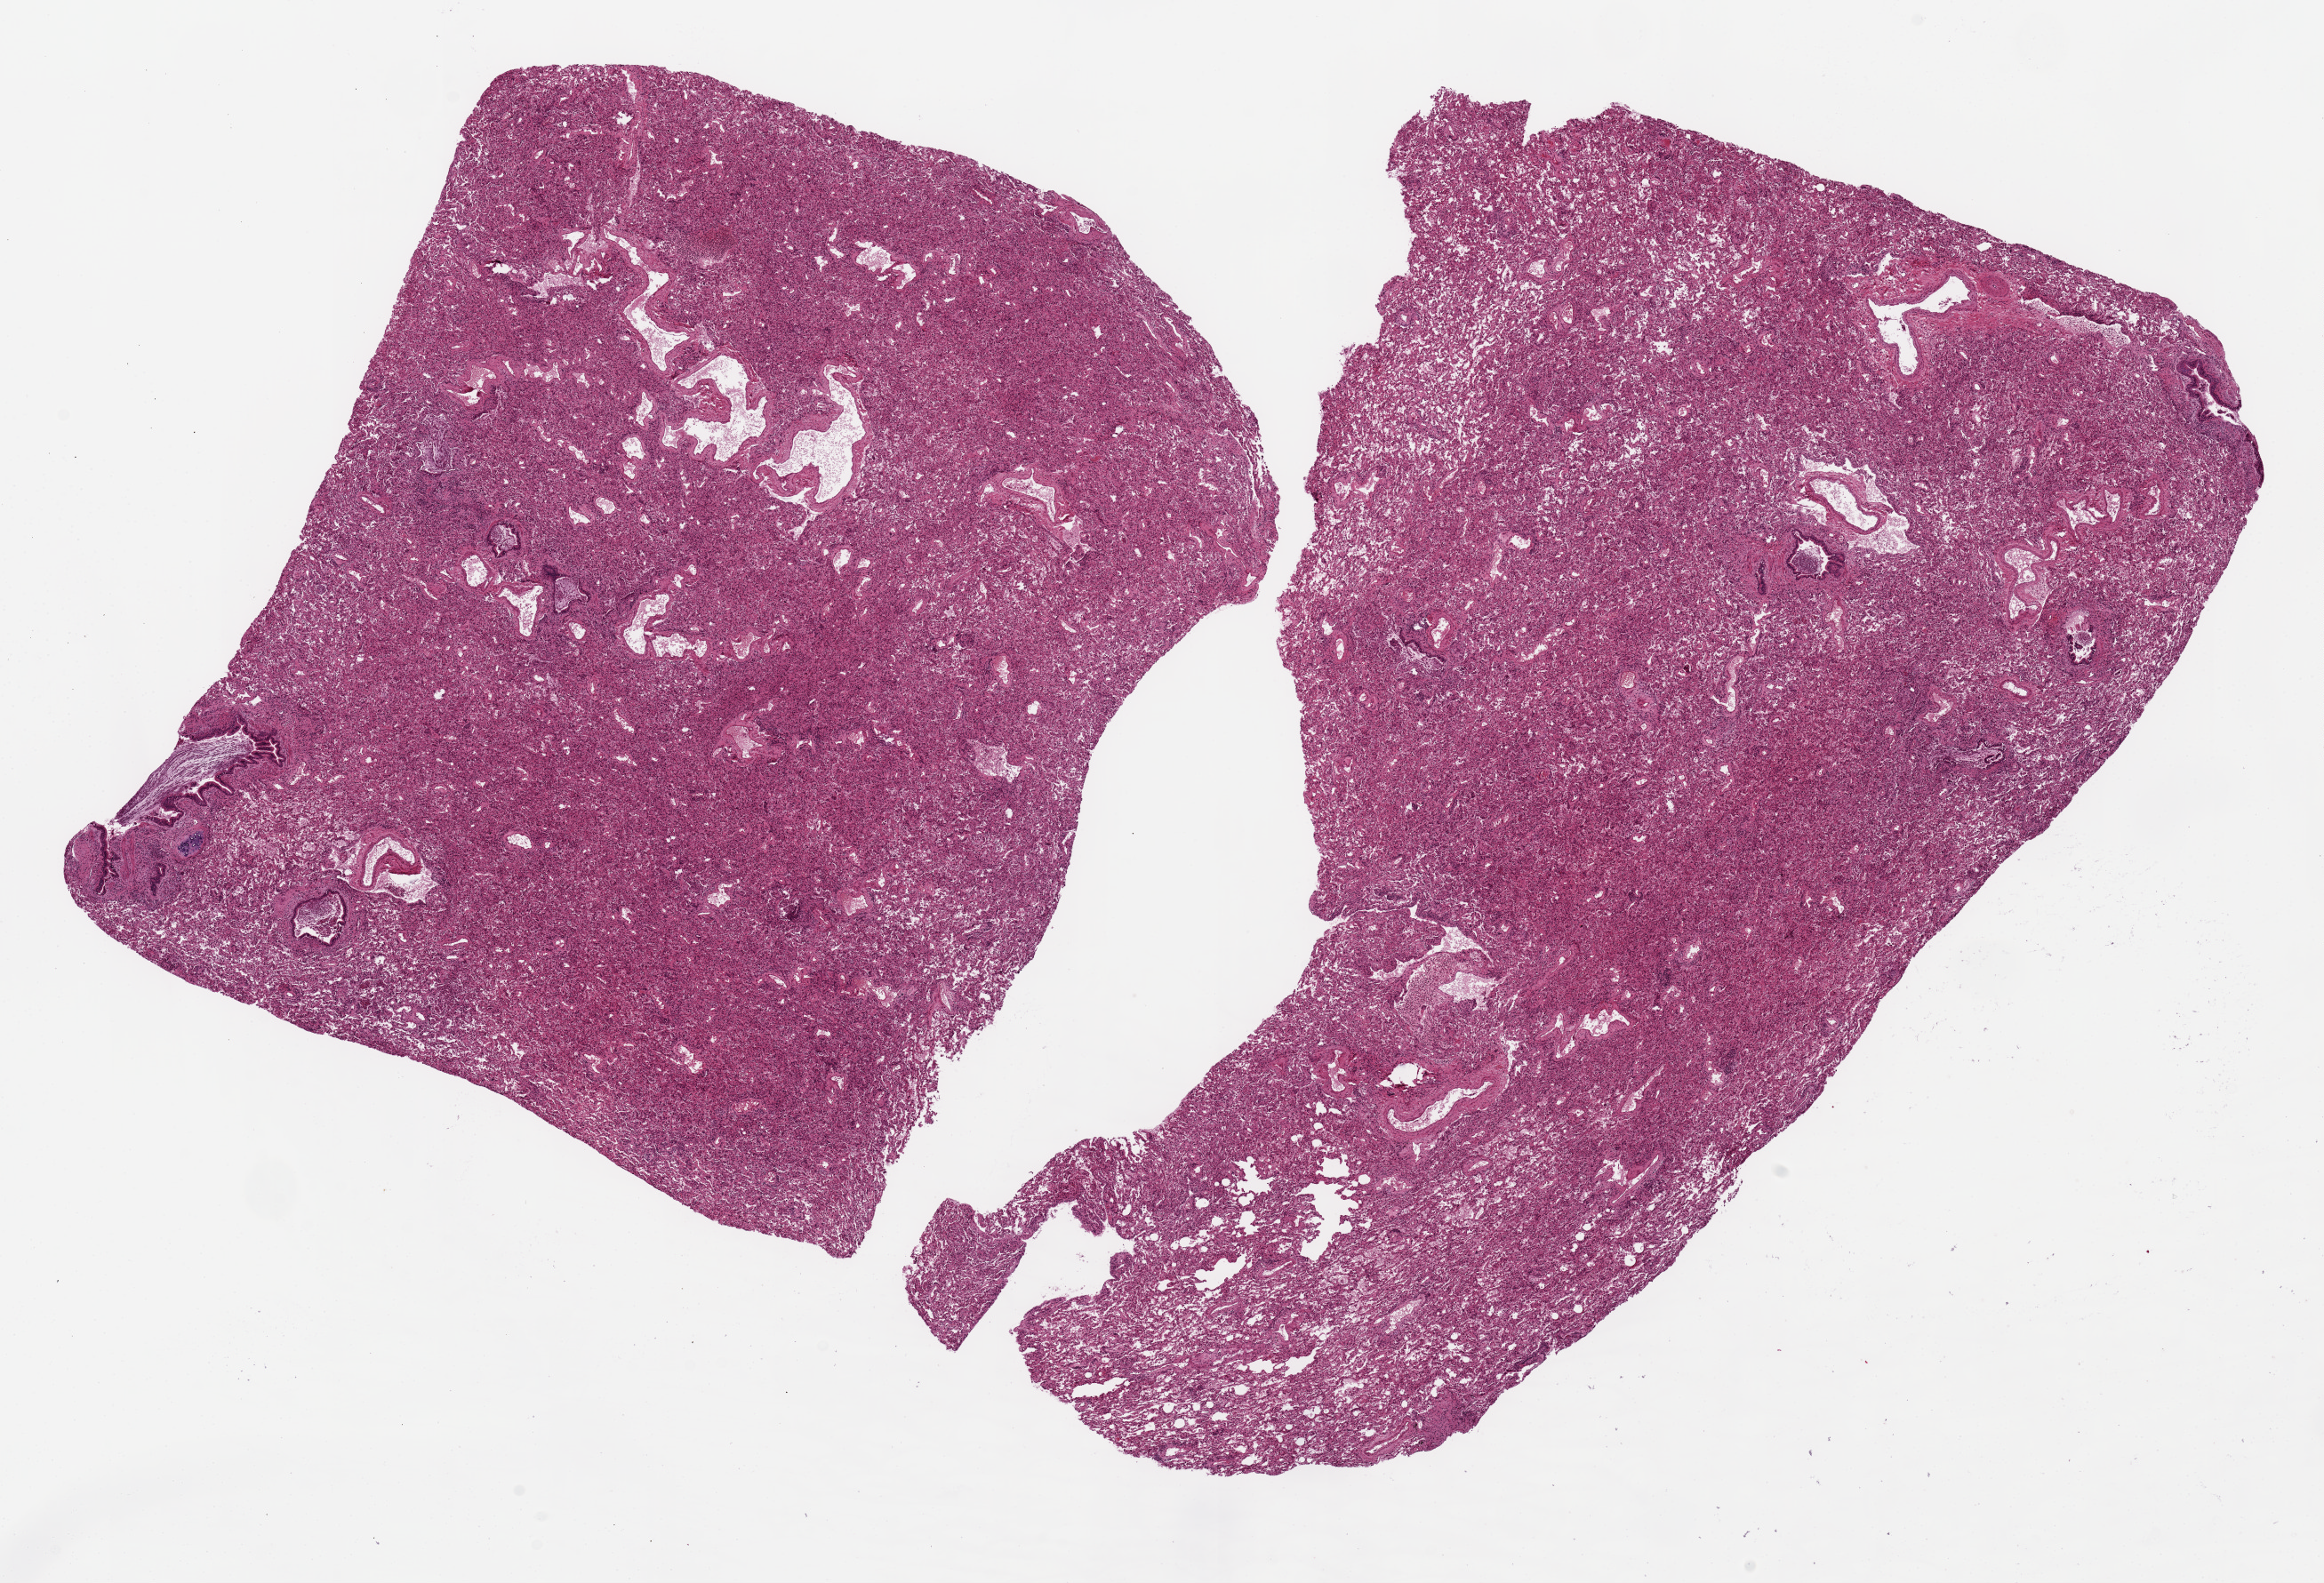
Hematoxylin and eosin (H&E) whole-slide image, brightfield, a low-resolution overview of the entire scanned area, about 20.7 x 14.1 mm; PAXgene-fixed, paraffin-embedded tissue; section of lung (target tissue); donor tissue sample. Donor sex: female.
- pathologist's review note for this sample: 2 ~11x8mm aliquots. Dense conolidation, pneumonia, fibrosis, pending glass review